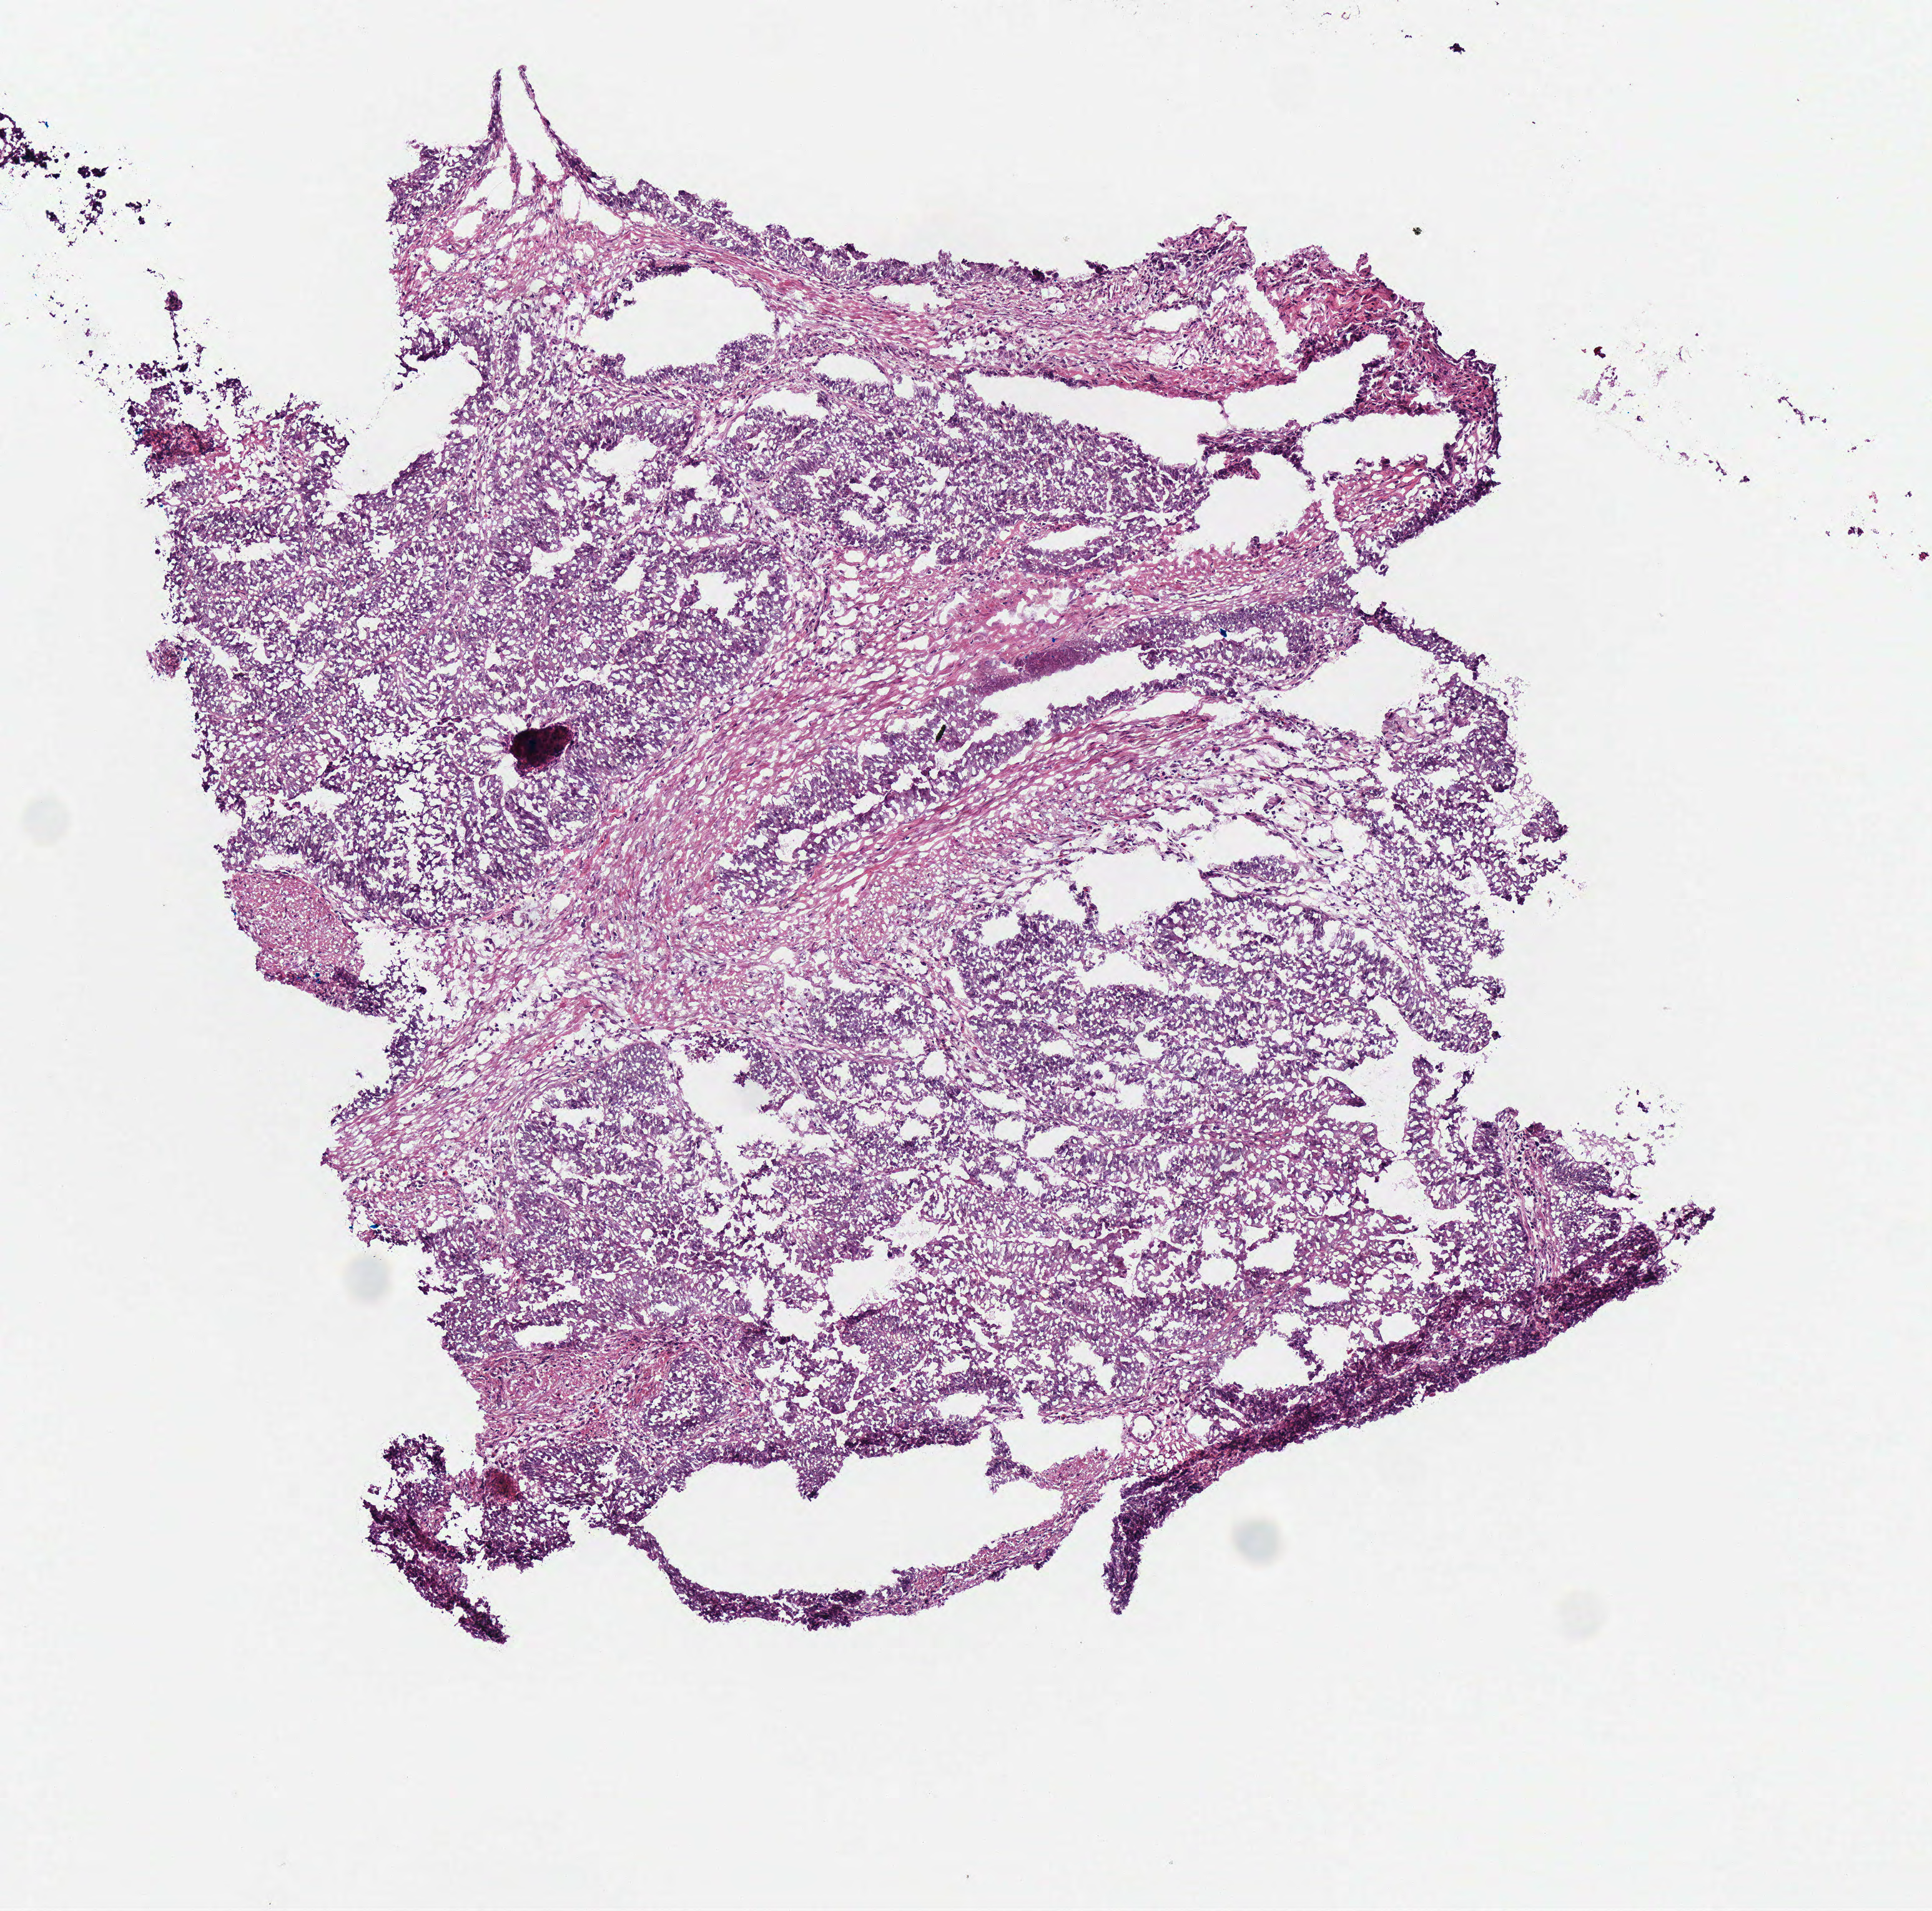
Hematoxylin and eosin (H&E) stained whole-slide image, low-resolution overview of the scanned area, about 3.0 x 3.0 mm. Frozen section from the bottom of the tissue portion. Primary tumour sample from the rectum. Male, age 48 years at initial diagnosis. Slide review estimates, as recorded: tumour cells 80%, tumour nuclei 85%, normal cells 0%, stromal cells 20%, necrosis 0%.
AJCC pathologic stage: I (7th edition). Lymph nodes positive (case pathology): 0 of 14 examined. Pathologic diagnosis: Adenocarcinoma, NOS (rectosigmoid junction).